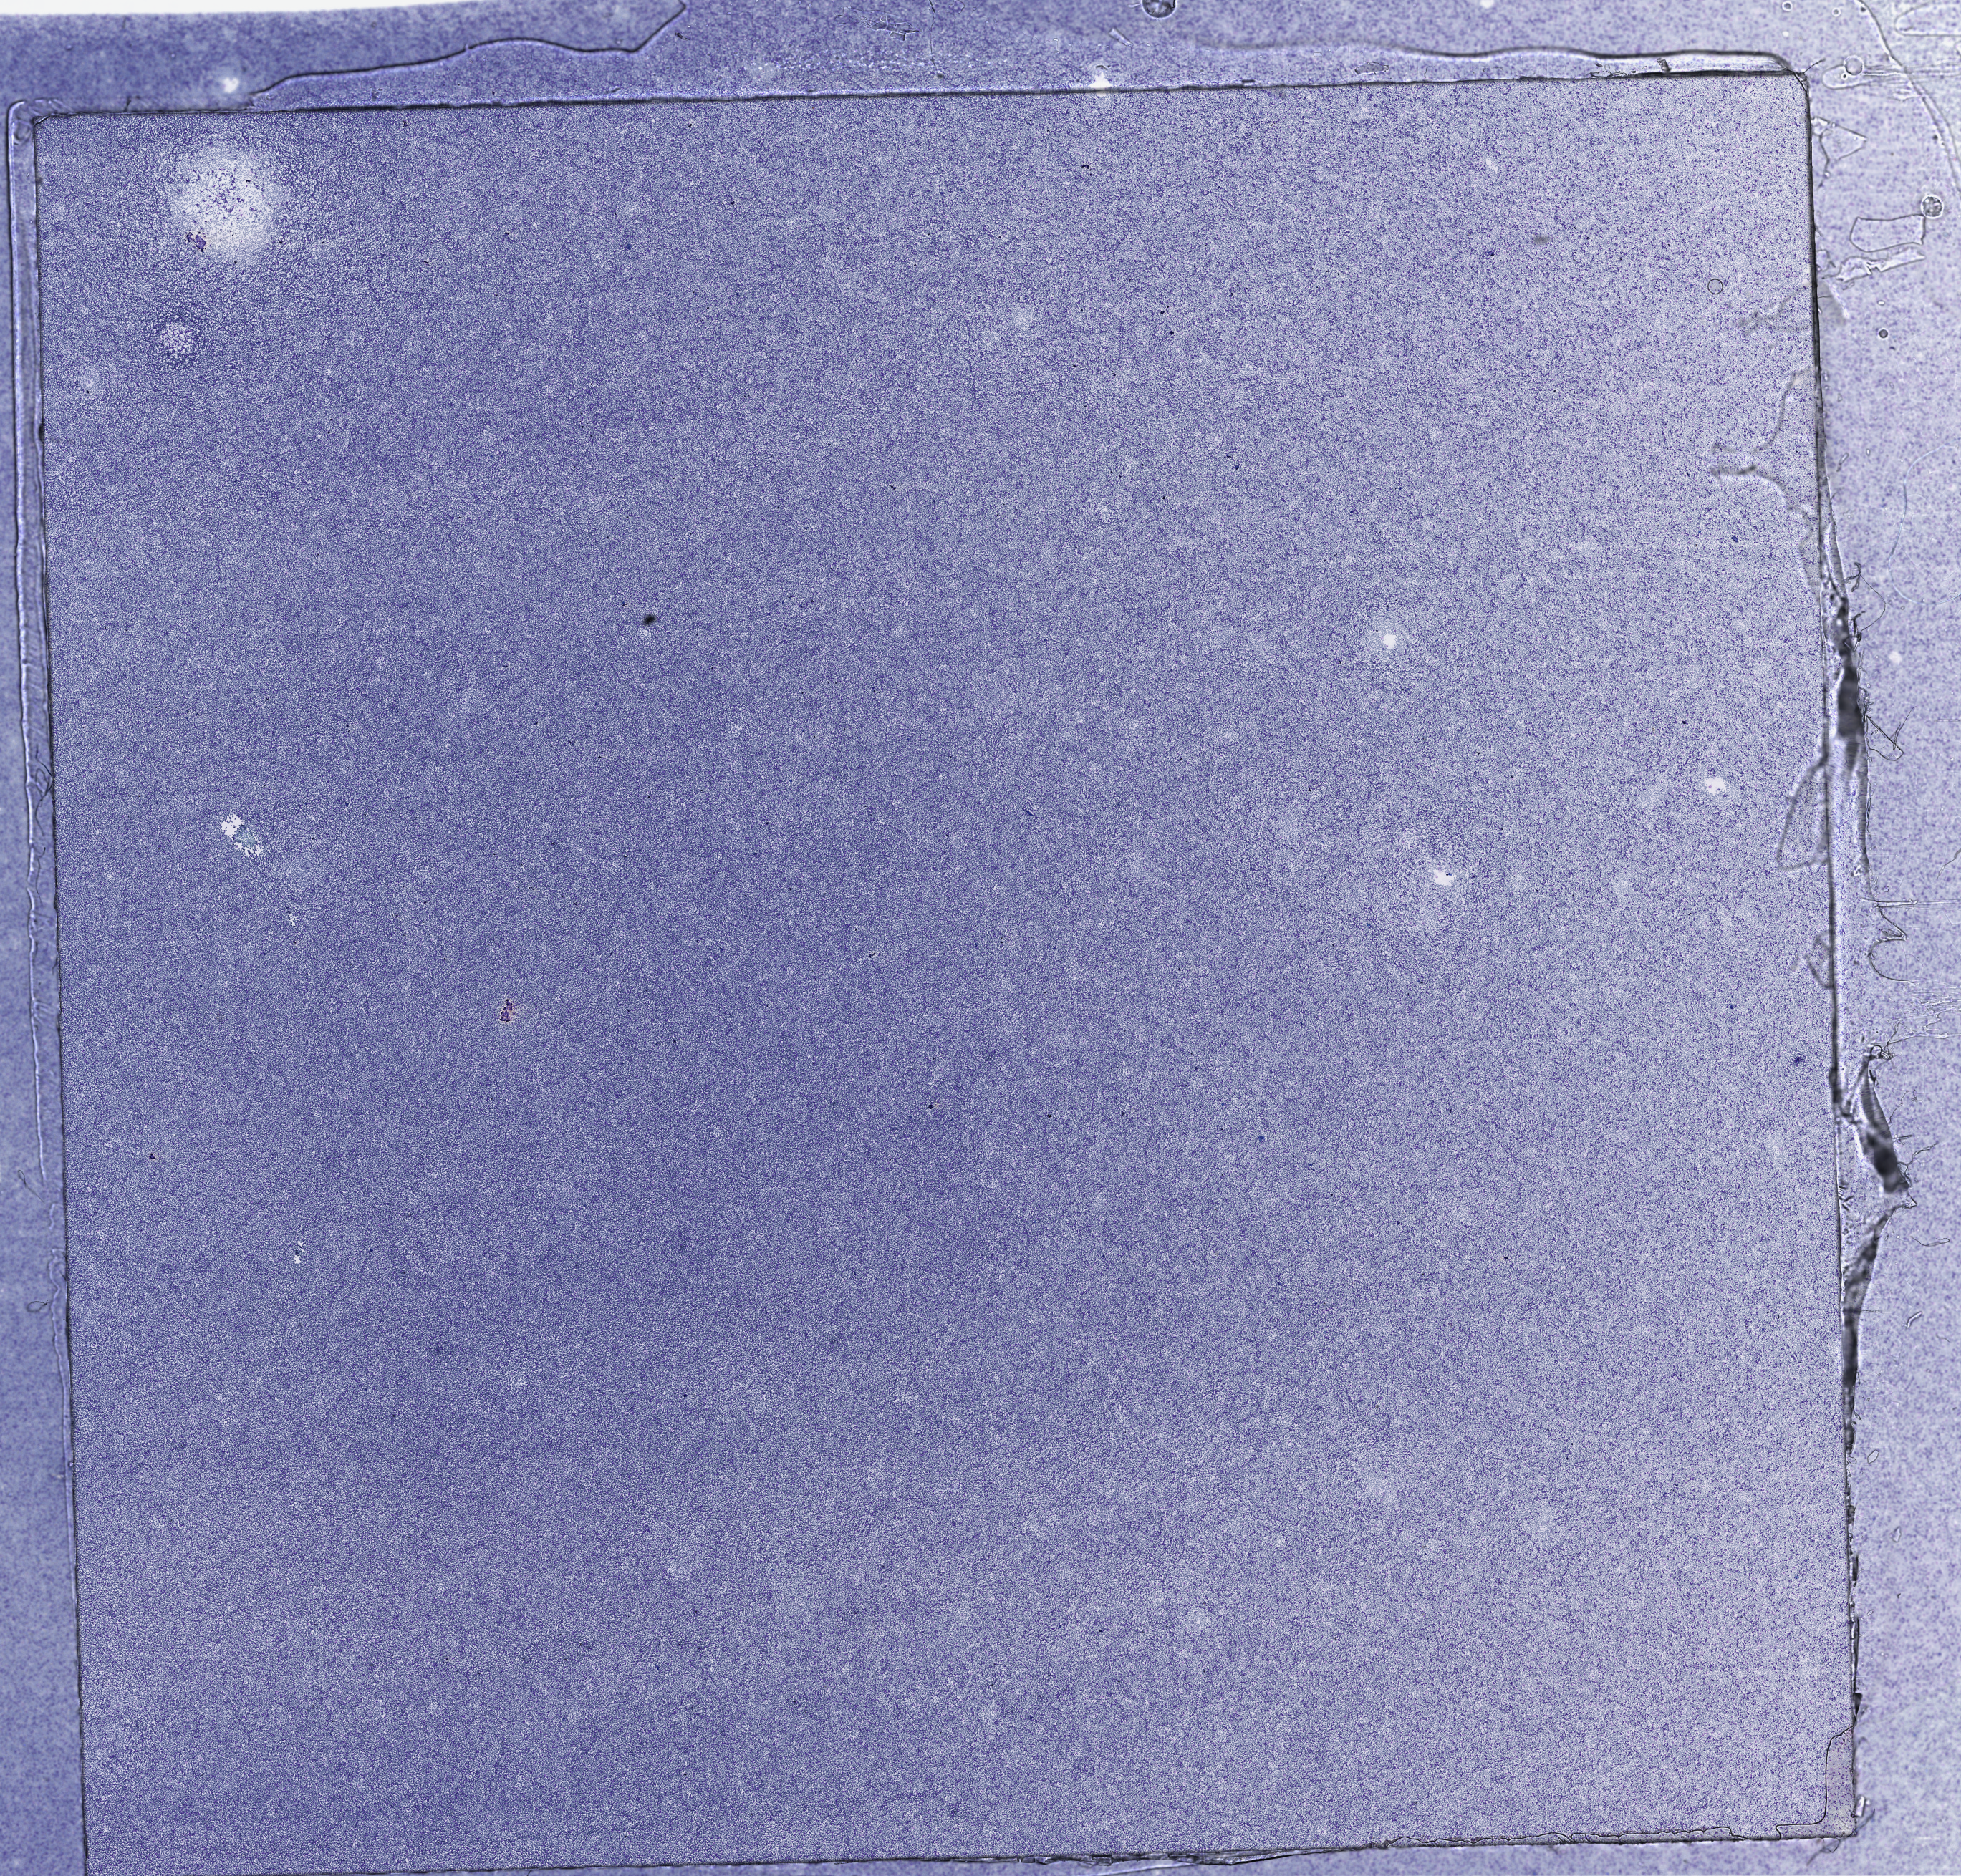
Whole-slide histology image, H&E-stained — shown as a low-resolution overview of the whole scanned area (about 22.1 x 21.2 mm, acquisition: 40x scan); peripheral blood (leukaemic) sample. 80-year-old female patient.
* diagnosis: Acute Myeloid Leukemia
* WHO classification: AML with minimal differentiation